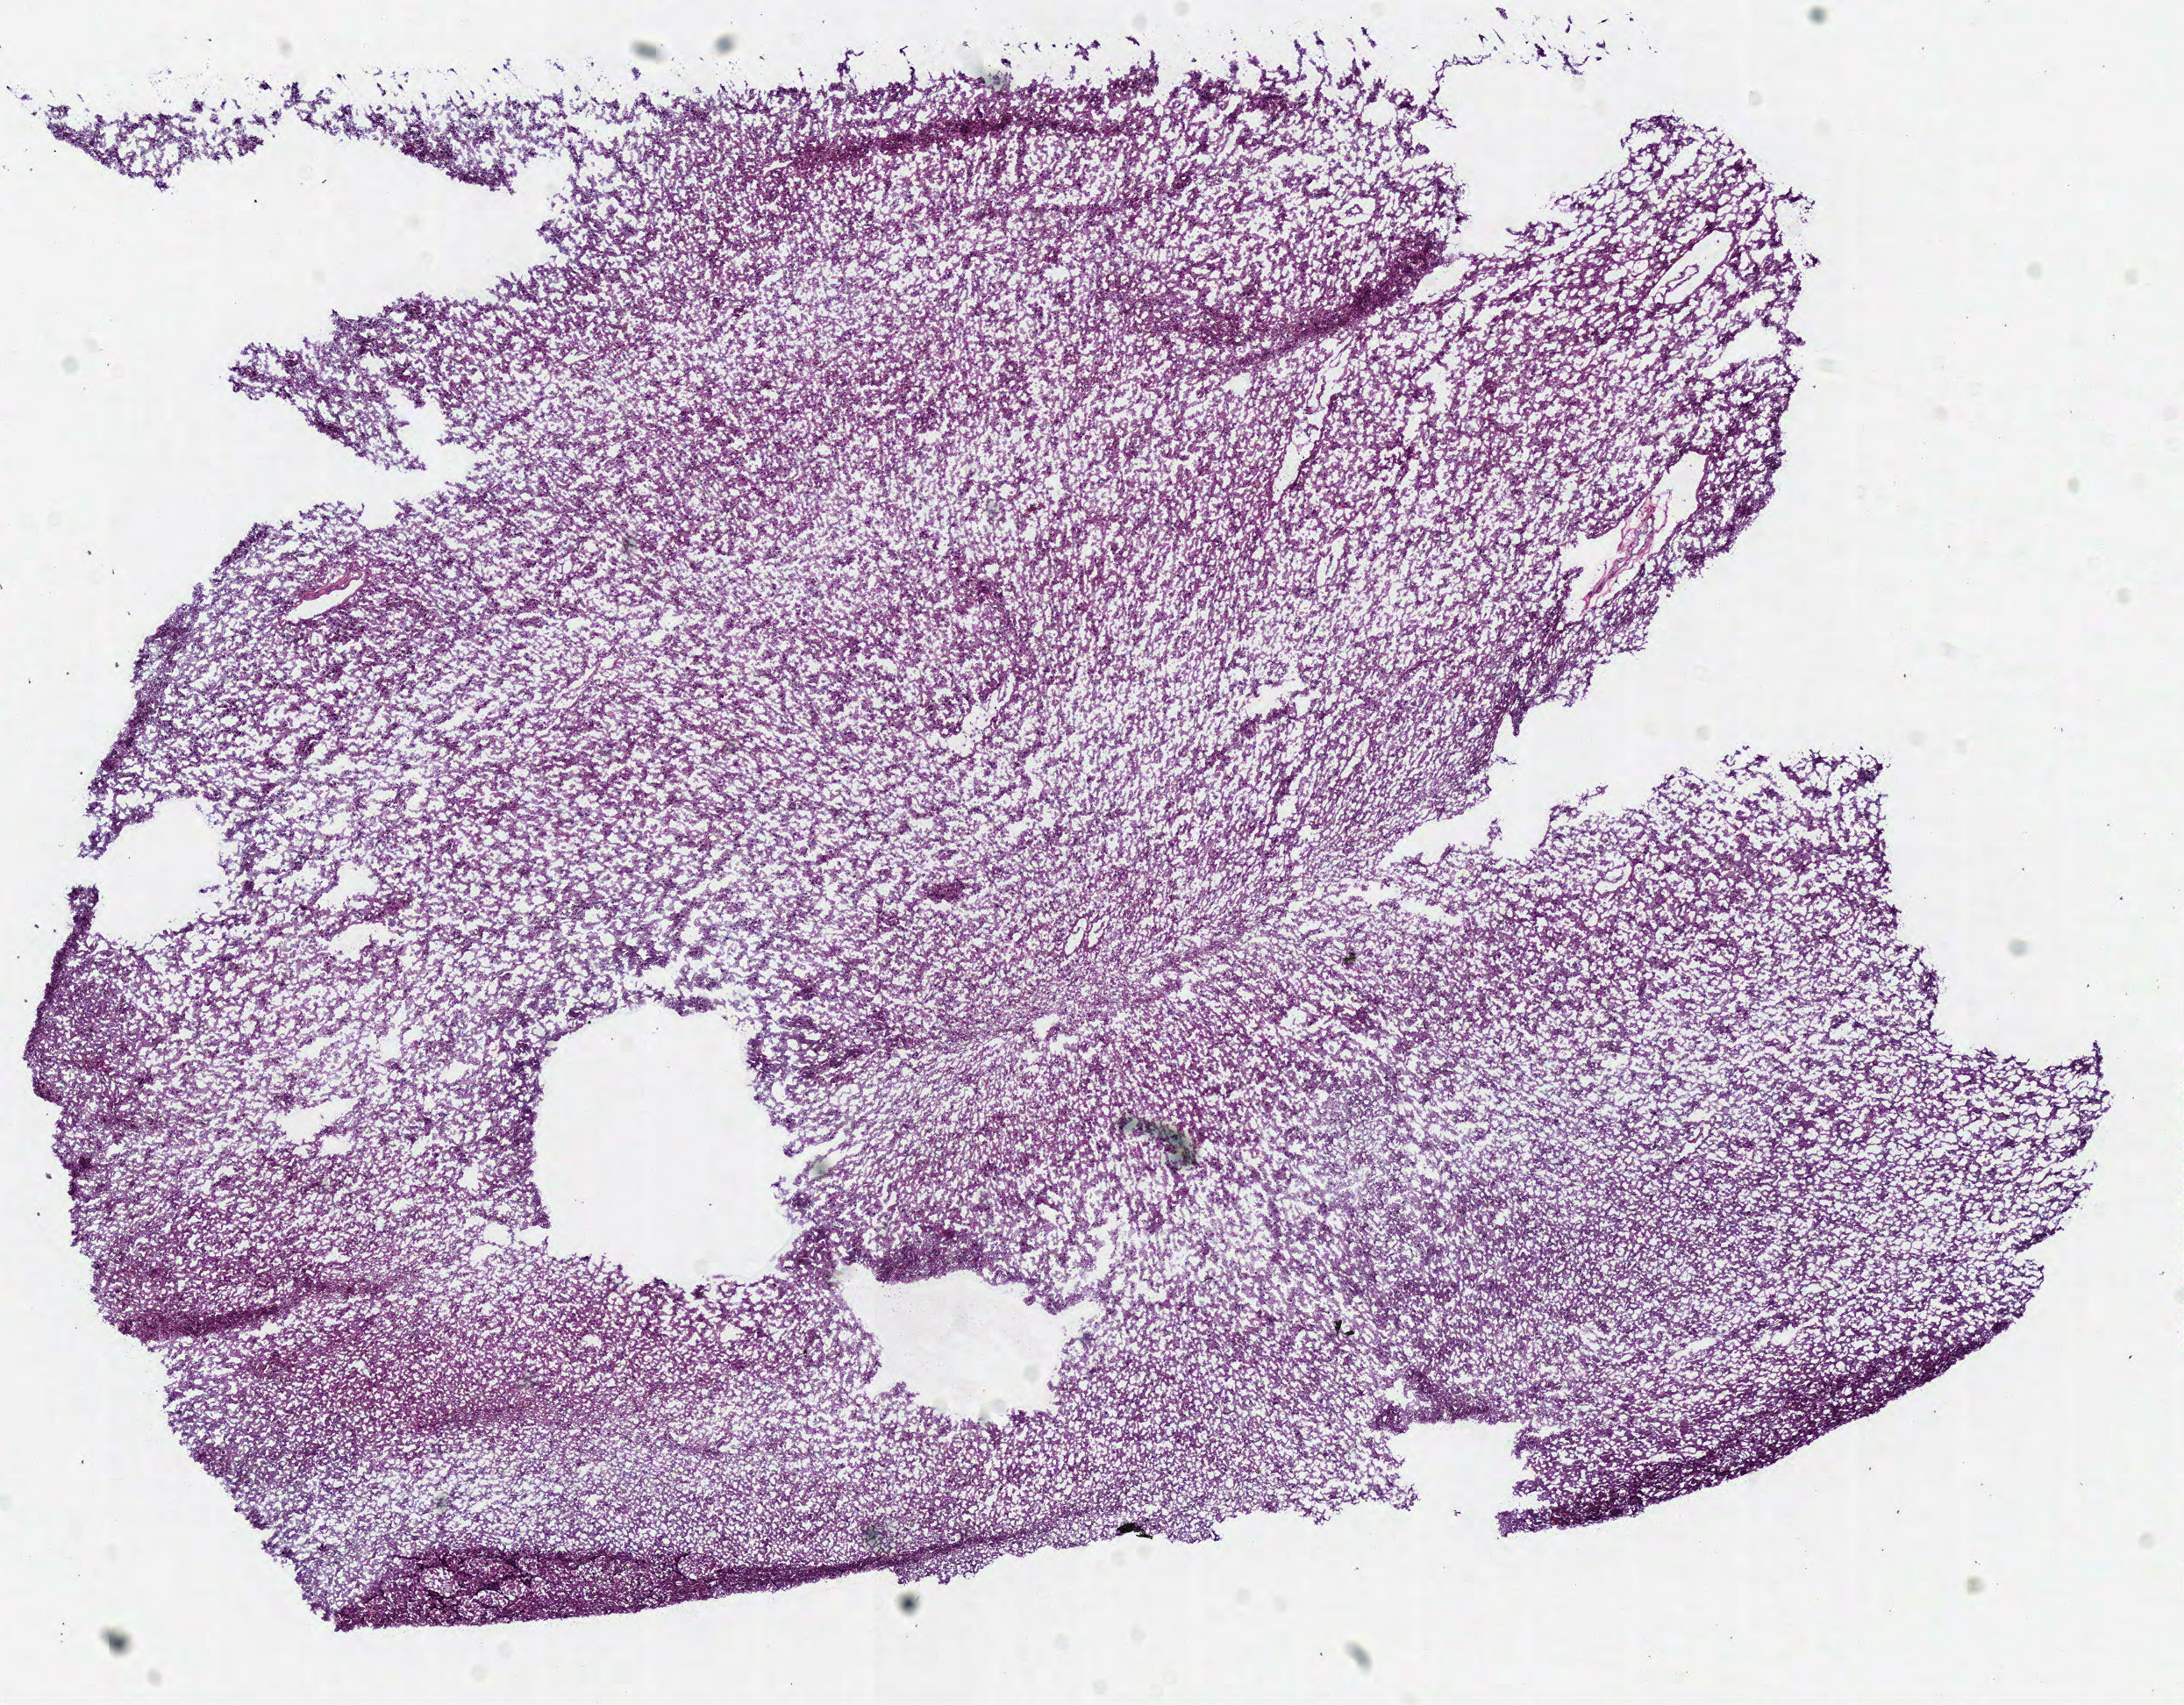
Digitized H&E-stained tissue section (whole slide), whole scanned area (about 9.8 x 7.6 mm) shown as a low-resolution overview, frozen section from the bottom of the tissue portion, brain, primary tumour sample. Male patient; age at initial diagnosis 30 years. Histologic grade: G2 (moderately differentiated). Pathologist review of this section (percent, as recorded): tumour cells 100%, tumour nuclei 70%, normal cells 0%, stromal cells 0%, necrosis 0%.
Pathologic diagnosis: Astrocytoma, NOS (cerebrum). Laterality: right.